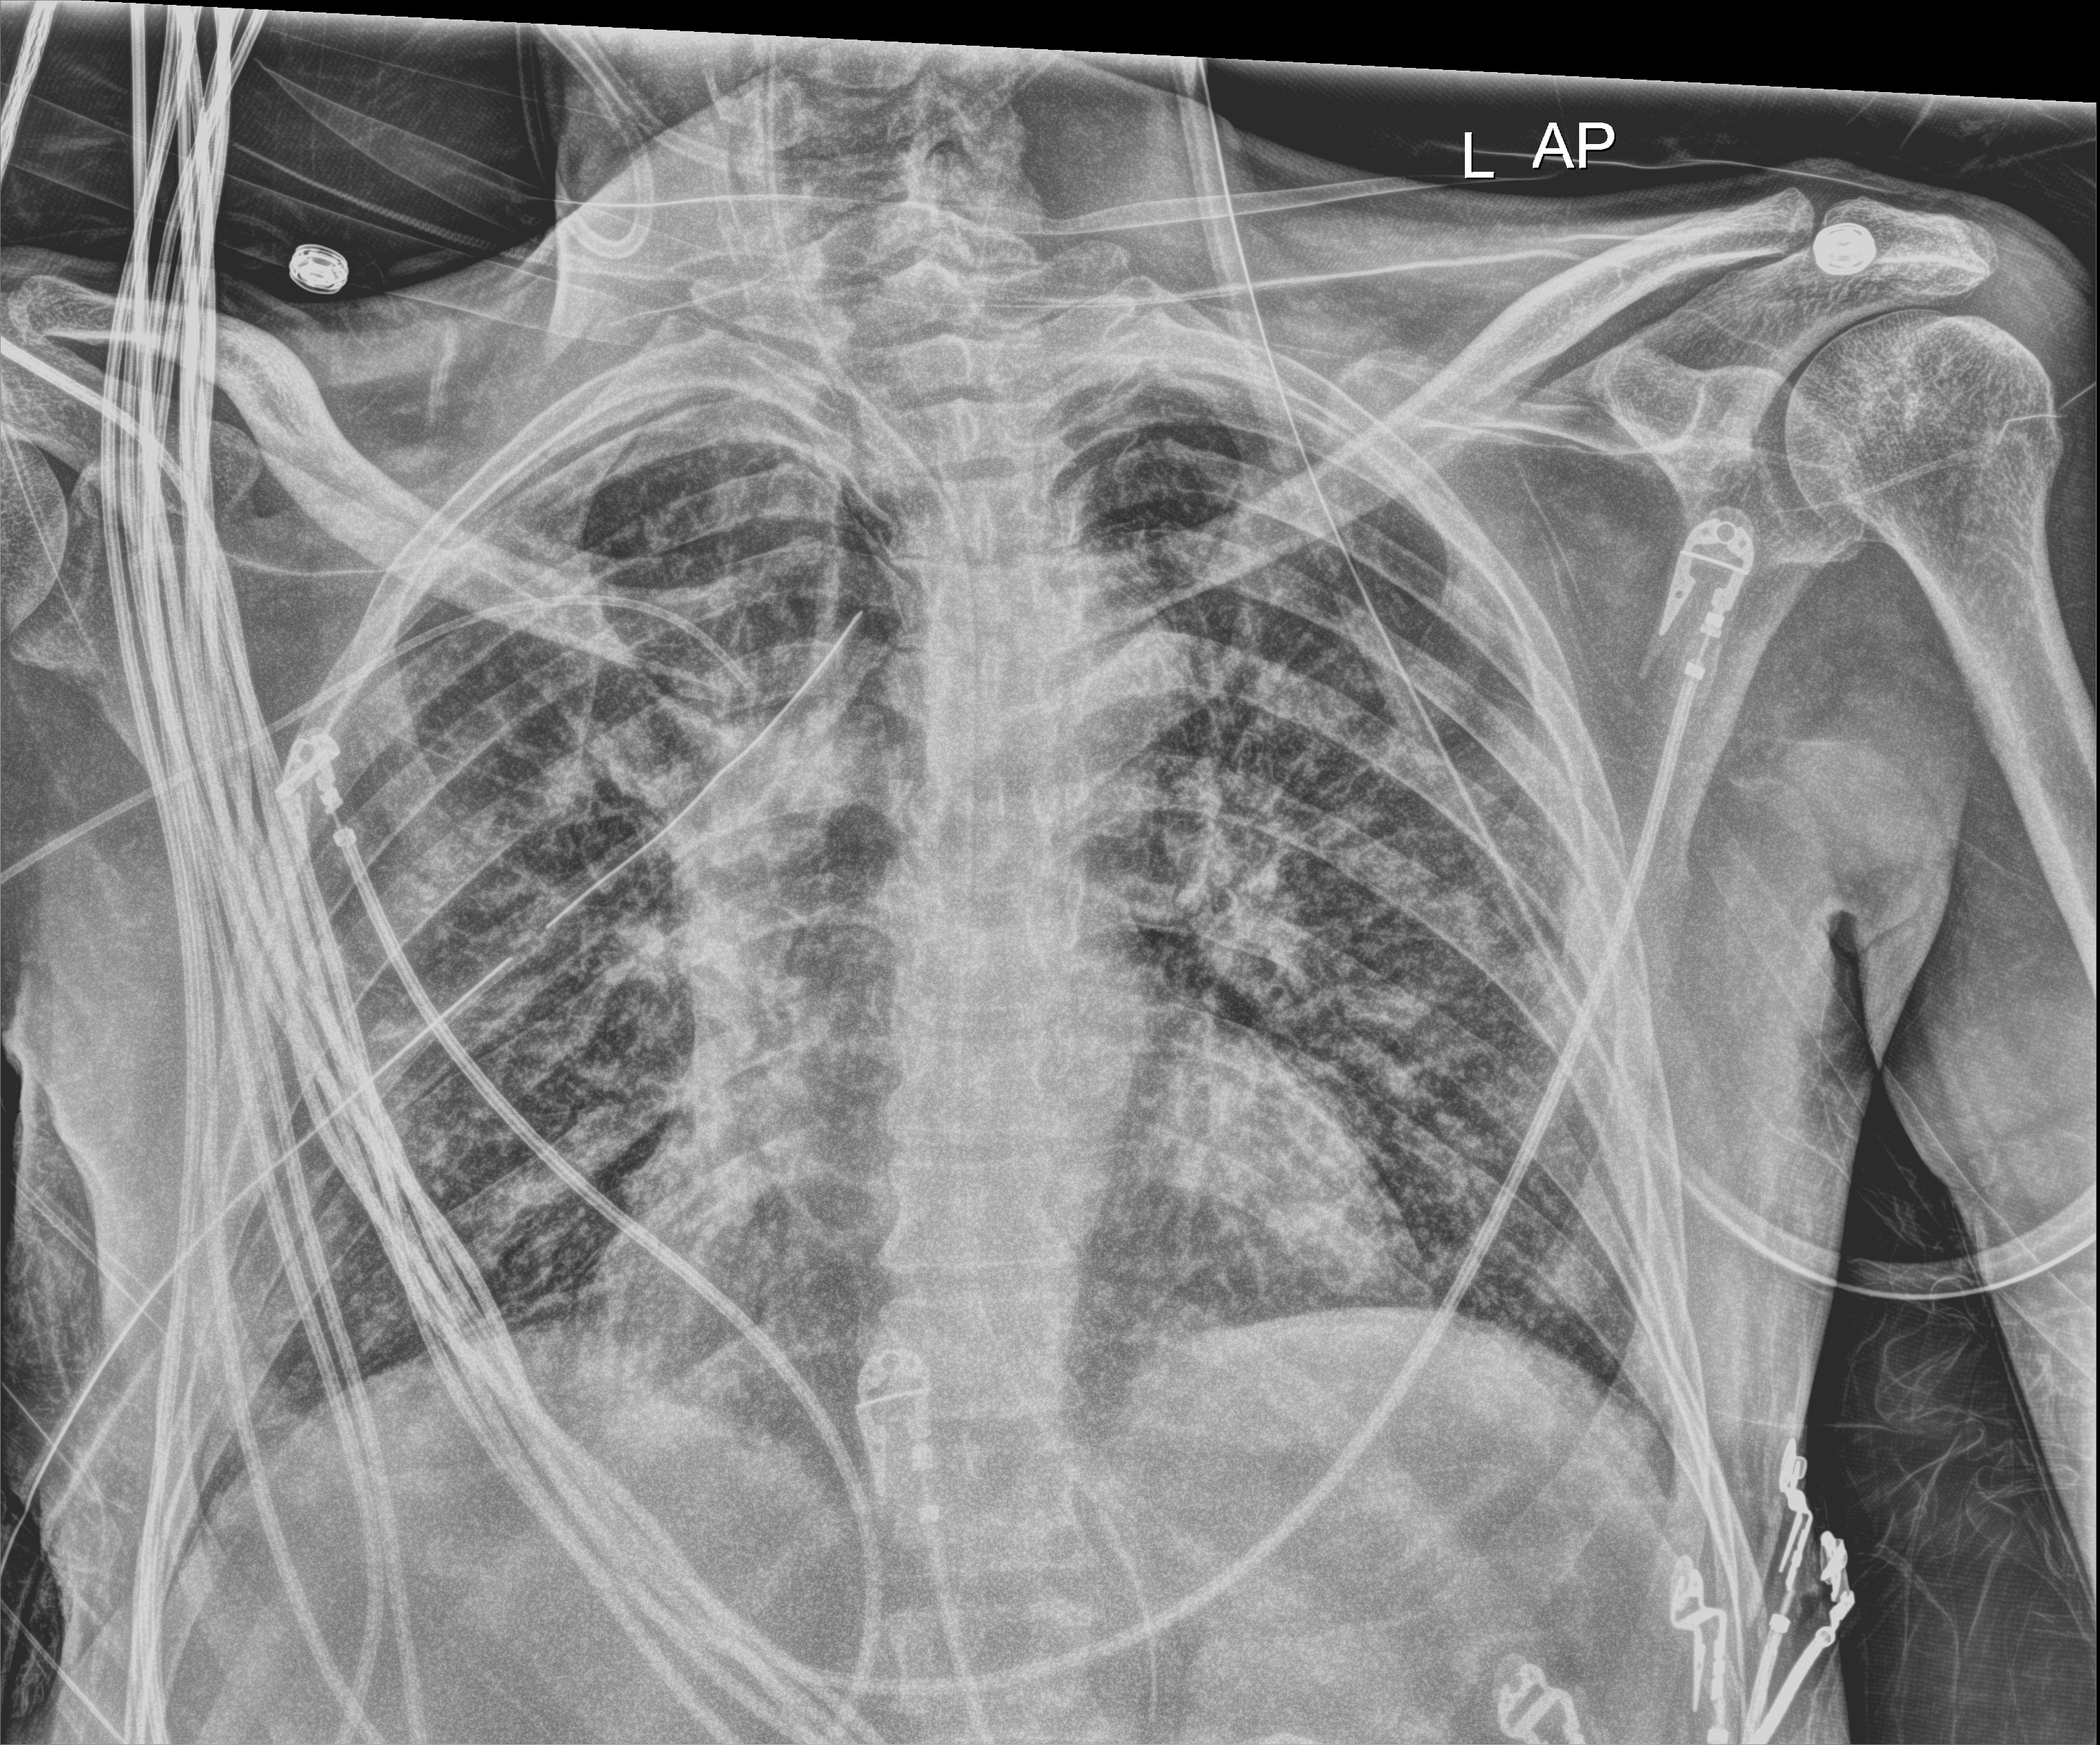
Chest X-ray (portable); anteroposterior (AP) projection. Male patient hospitalised with COVID-19, age 18–59 years.
Admission-level facts for this patient (not findings on this image; timing relative to this image not recorded): length of hospital stay: 41 days; other chronic lung disease (admission record): no; mechanically ventilated during this hospital stay: yes.